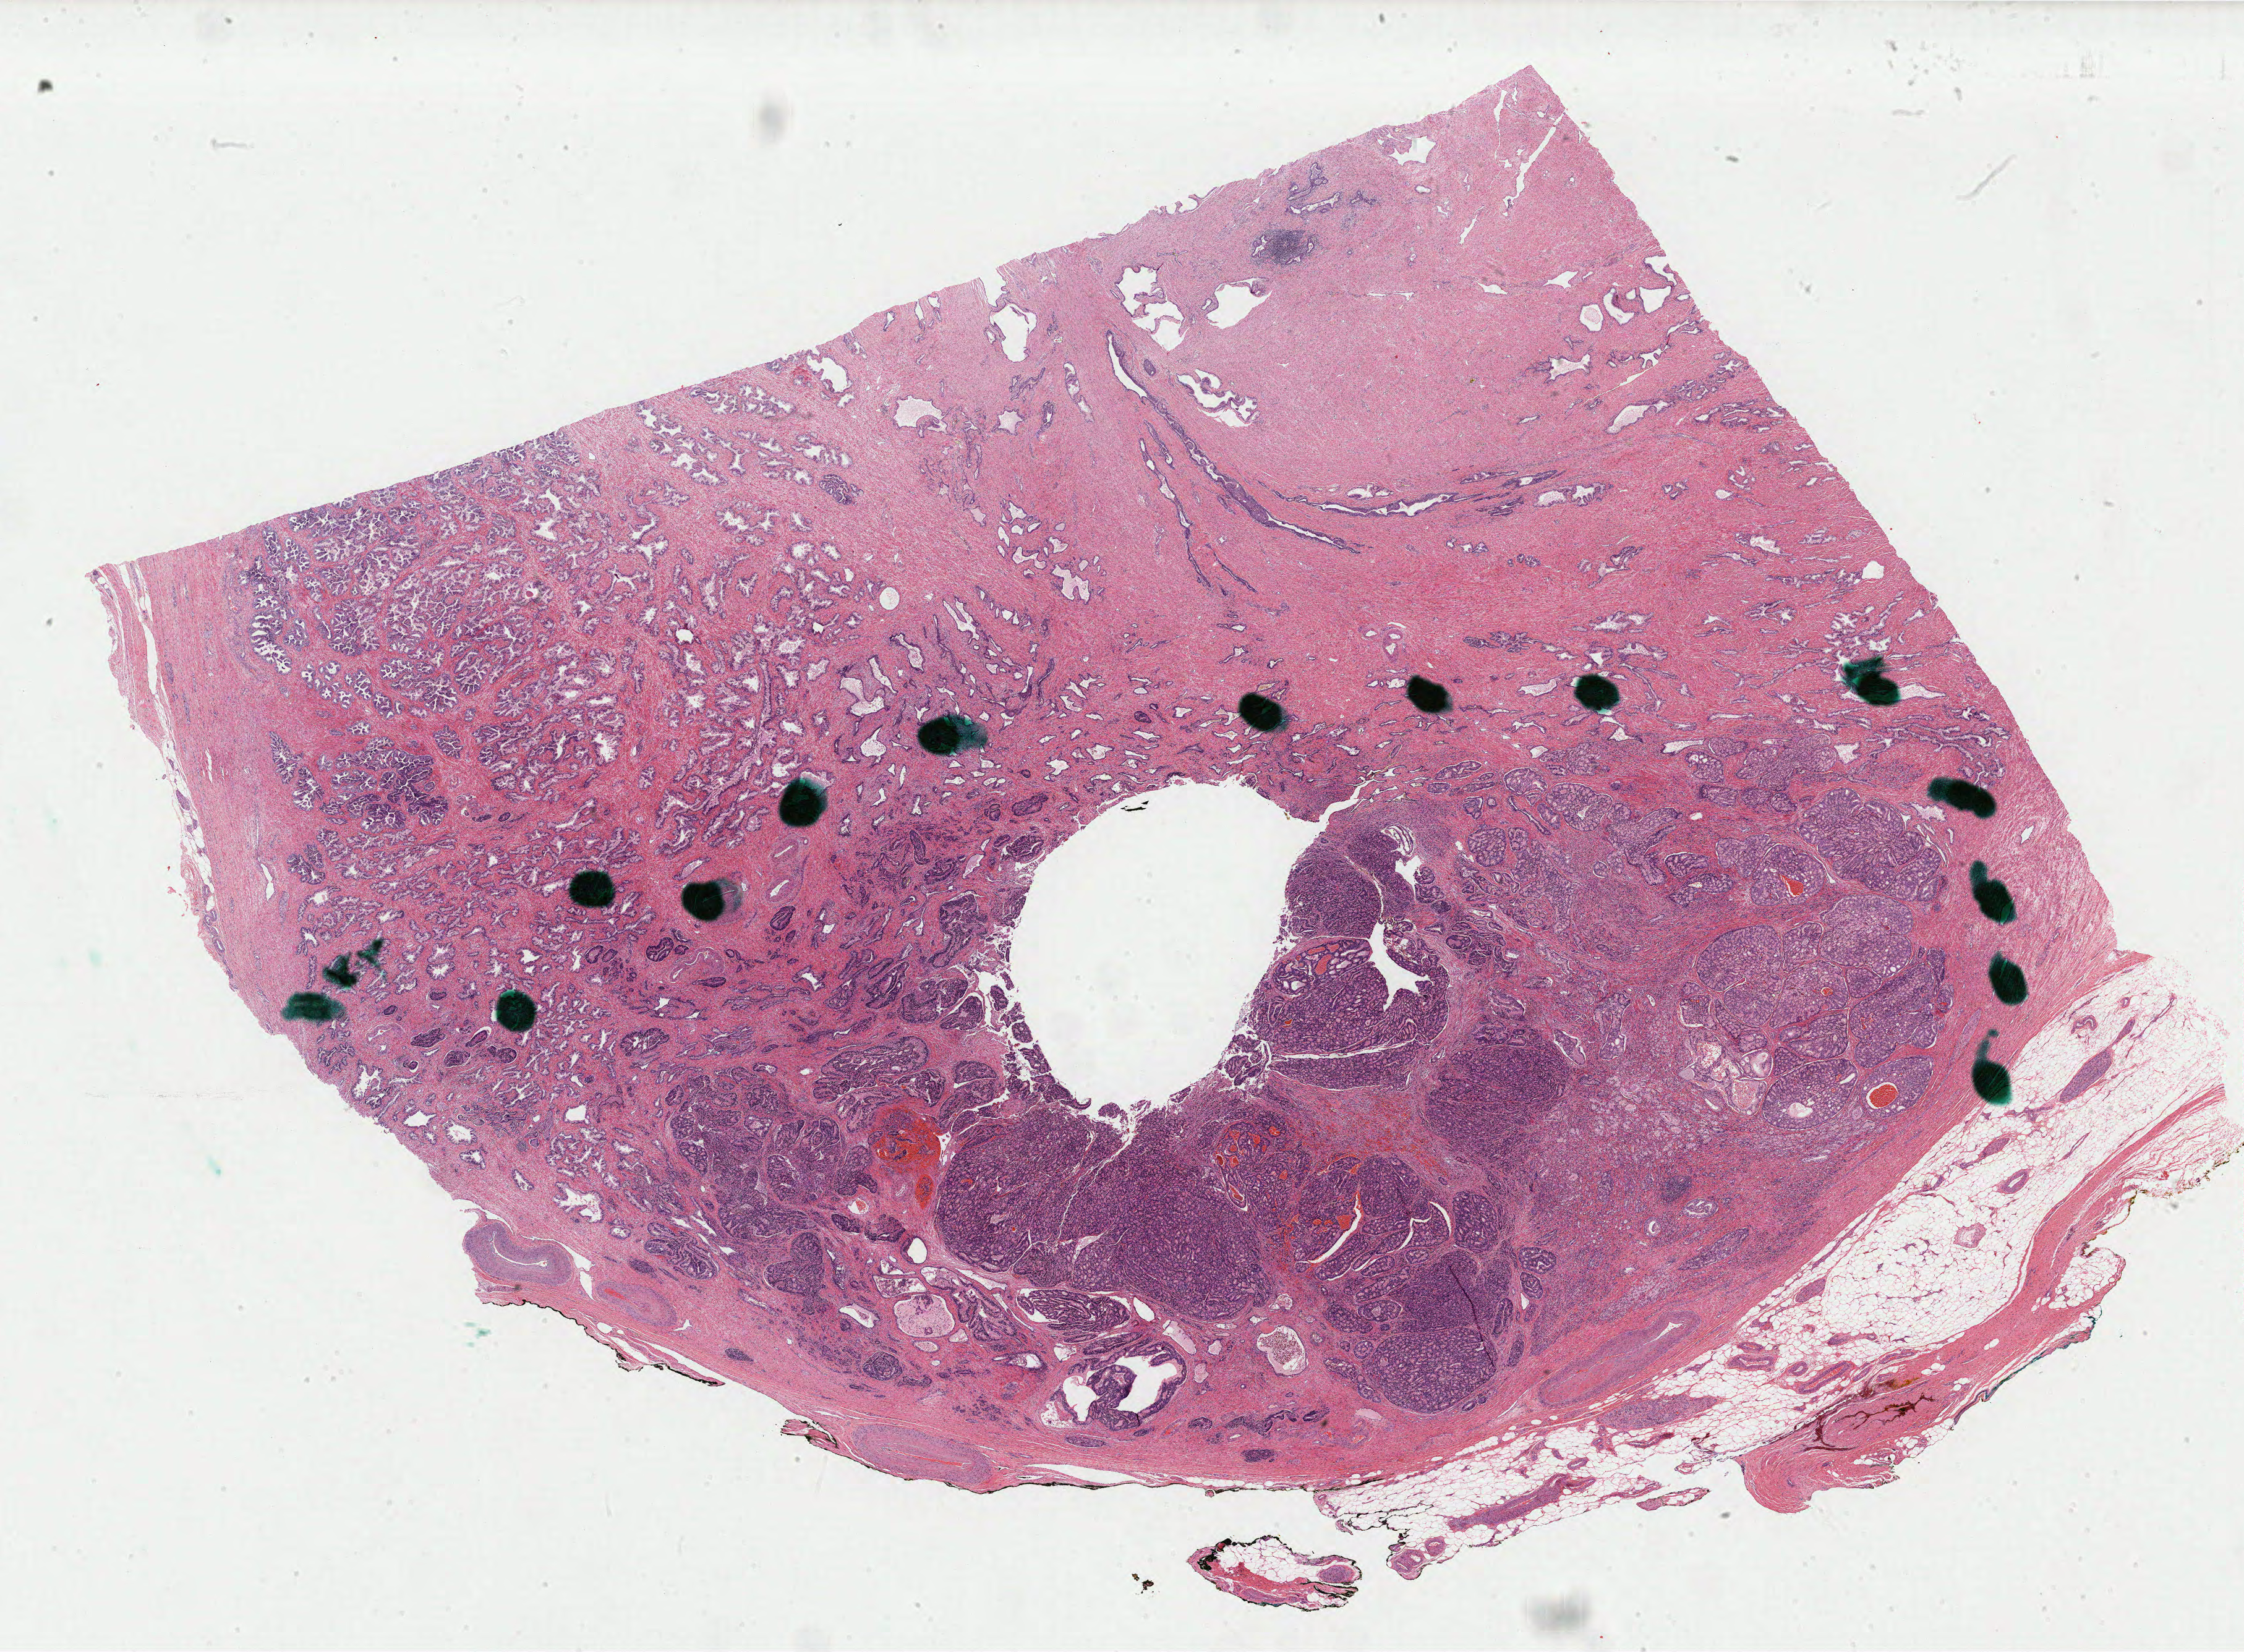
Whole-slide histology image, H&E-stained, whole scanned area (about 28.8 x 21.2 mm, slide scanned at 40x) shown as a low-resolution overview. Formalin-fixed paraffin-embedded (FFPE) diagnostic section. Prostate, primary tumour sample. Male, age 56 years at initial diagnosis.
Diagnosis: Adenocarcinoma, NOS (prostate gland).